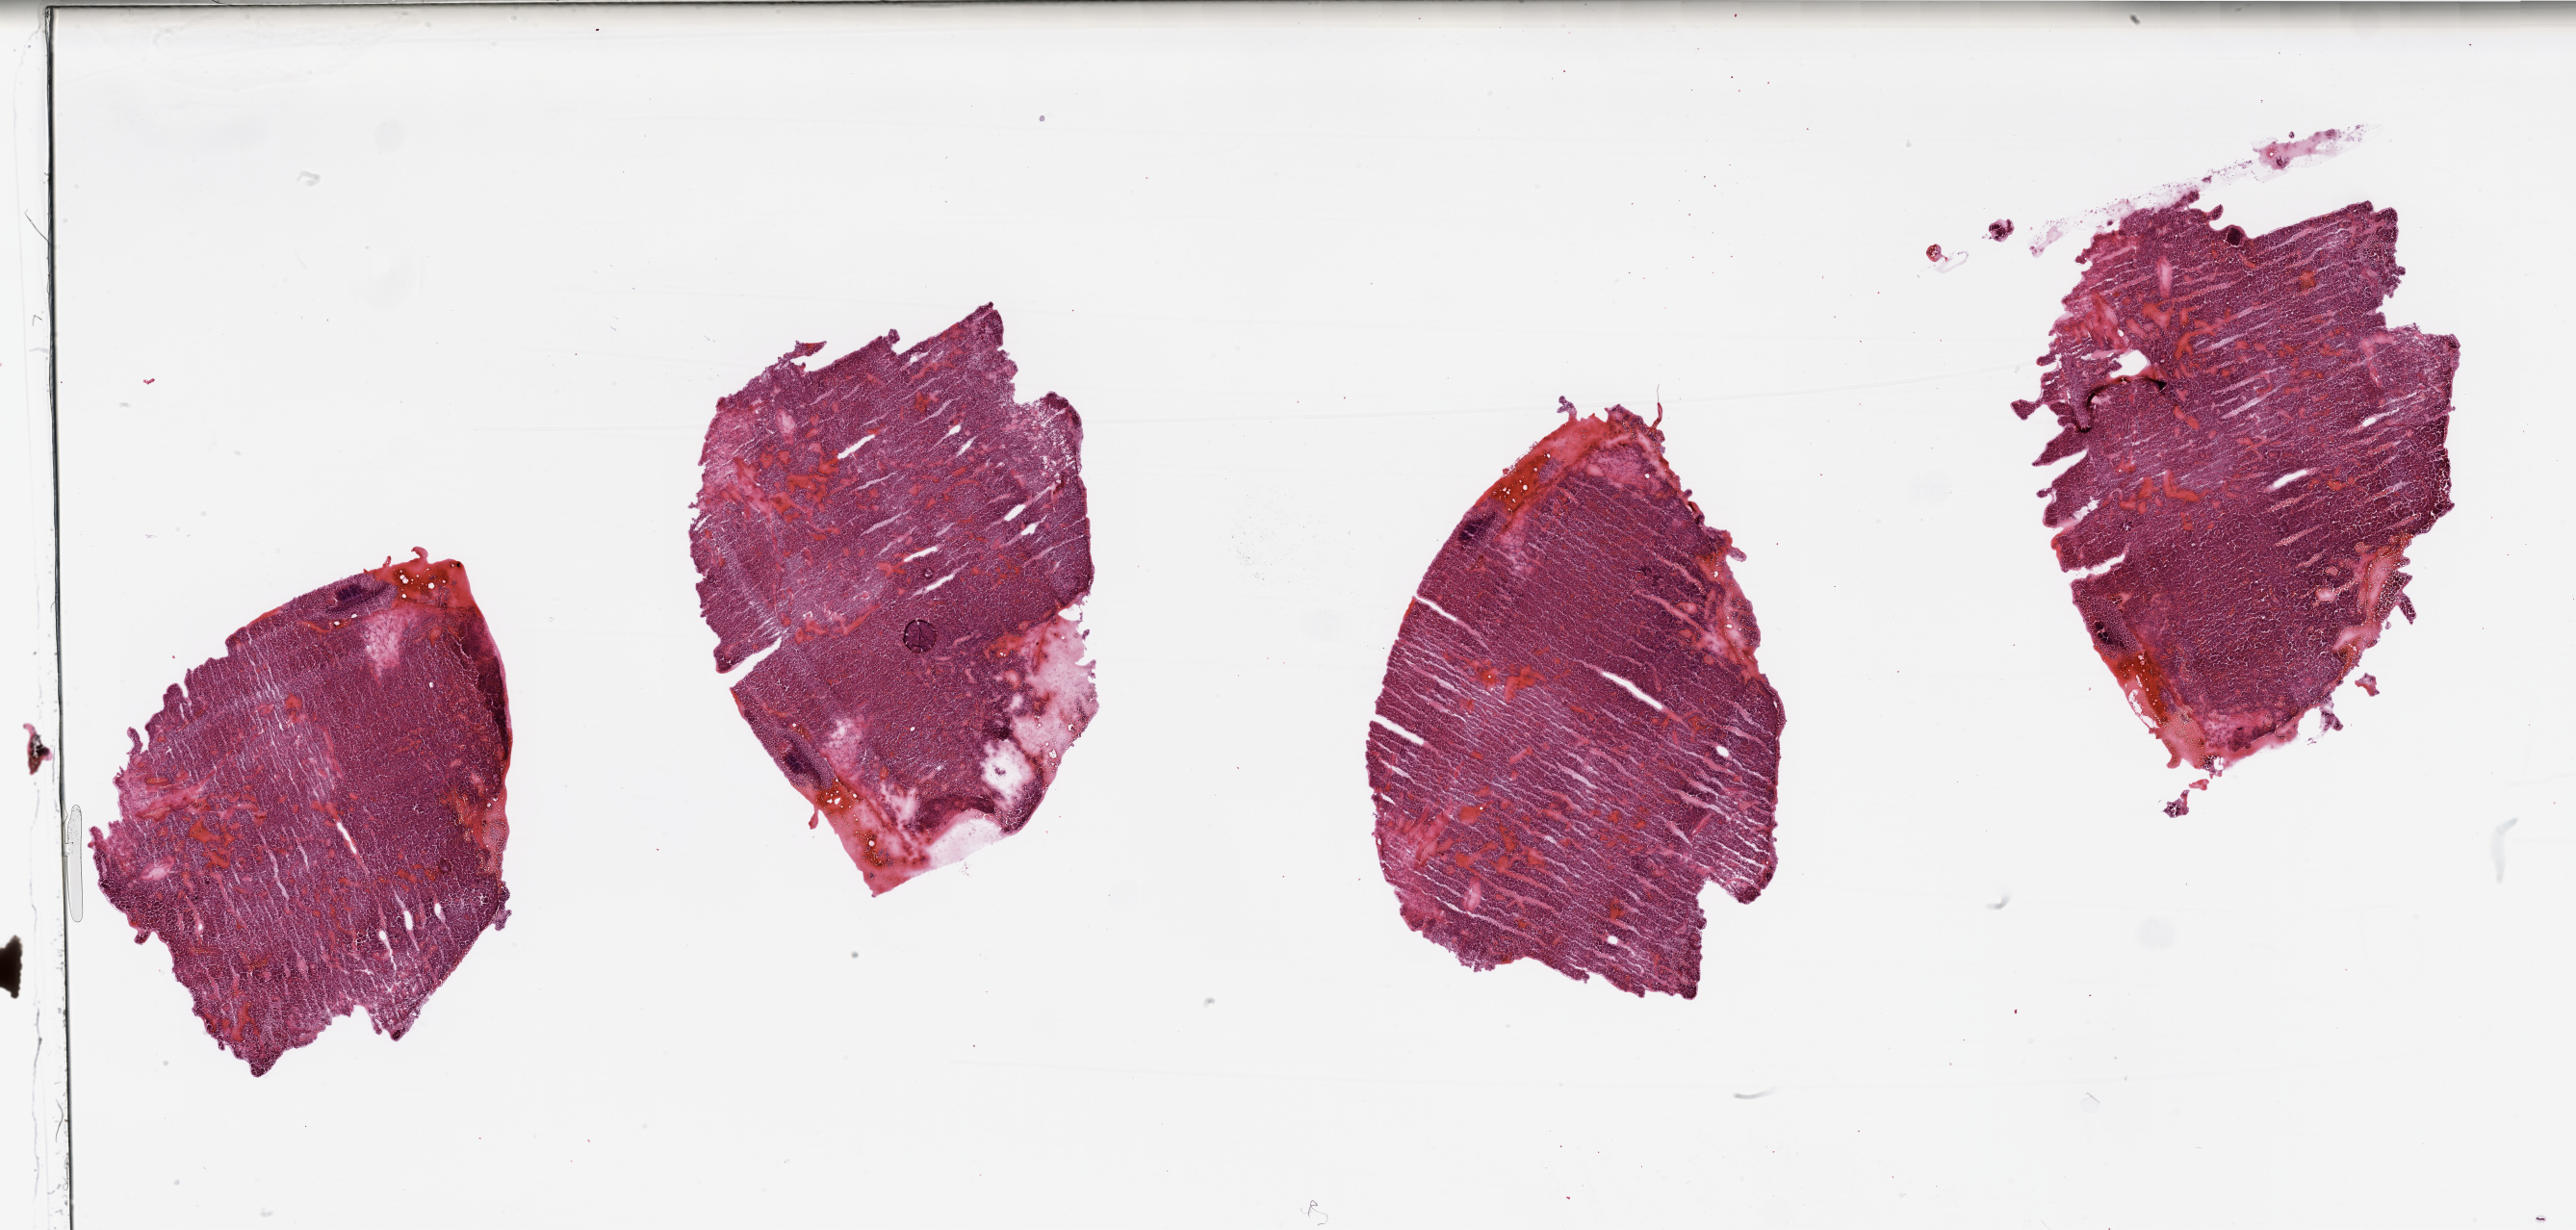
Digitized H&E-stained tissue section (whole slide) — a low-resolution overview of the entire scanned area, about 42.3 x 20.2 mm. Tumour tissue sample, sampled site: kidney. Patient: male, age 84 years. Histologic grade: G2 (moderately differentiated). Slide review estimates, as recorded: tumour nuclei 90%, necrosis 5%.
Primary tumour site (as recorded): upper pole. AJCC pathologic stage: III. Diagnosis: Renal cell carcinoma, NOS.